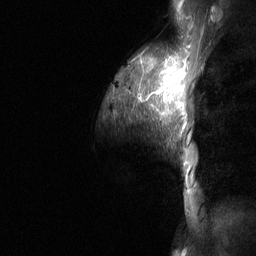
Breast MRI (dynamic contrast-enhanced), one sagittal slice. Slice 49 of 64 in the series (ordered by position). Dynamic contrast-enhanced study with each time point stored as its own series, time point 2 of 3 at this slice position (early post-contrast, ordered by acquisition time). 1.5 T. TE 4.8 ms, TR 27 ms. 2 mm slice thickness. 256 × 256 image matrix, field of view 200 × 200 mm. Female patient, age 36 years. Case-level facts recorded for this patient, not image findings: setting: breast cancer imaged before/during neoadjuvant chemotherapy; receptor status: HR-positive, HER2-negative.
Outlined on this slice (semi-automatic segmentation, software-assisted and operator-edited):
- analysis volume of interest (the breast-tissue region the enhancement analysis was run in; not a lesion): bounding box (x1, y1, x2, y2) in pixels: (110, 49, 187, 210)
- tumour enhancement mask (voxels above the 90 % enhancement threshold inside the analysis volume of interest): (139, 60, 187, 115)